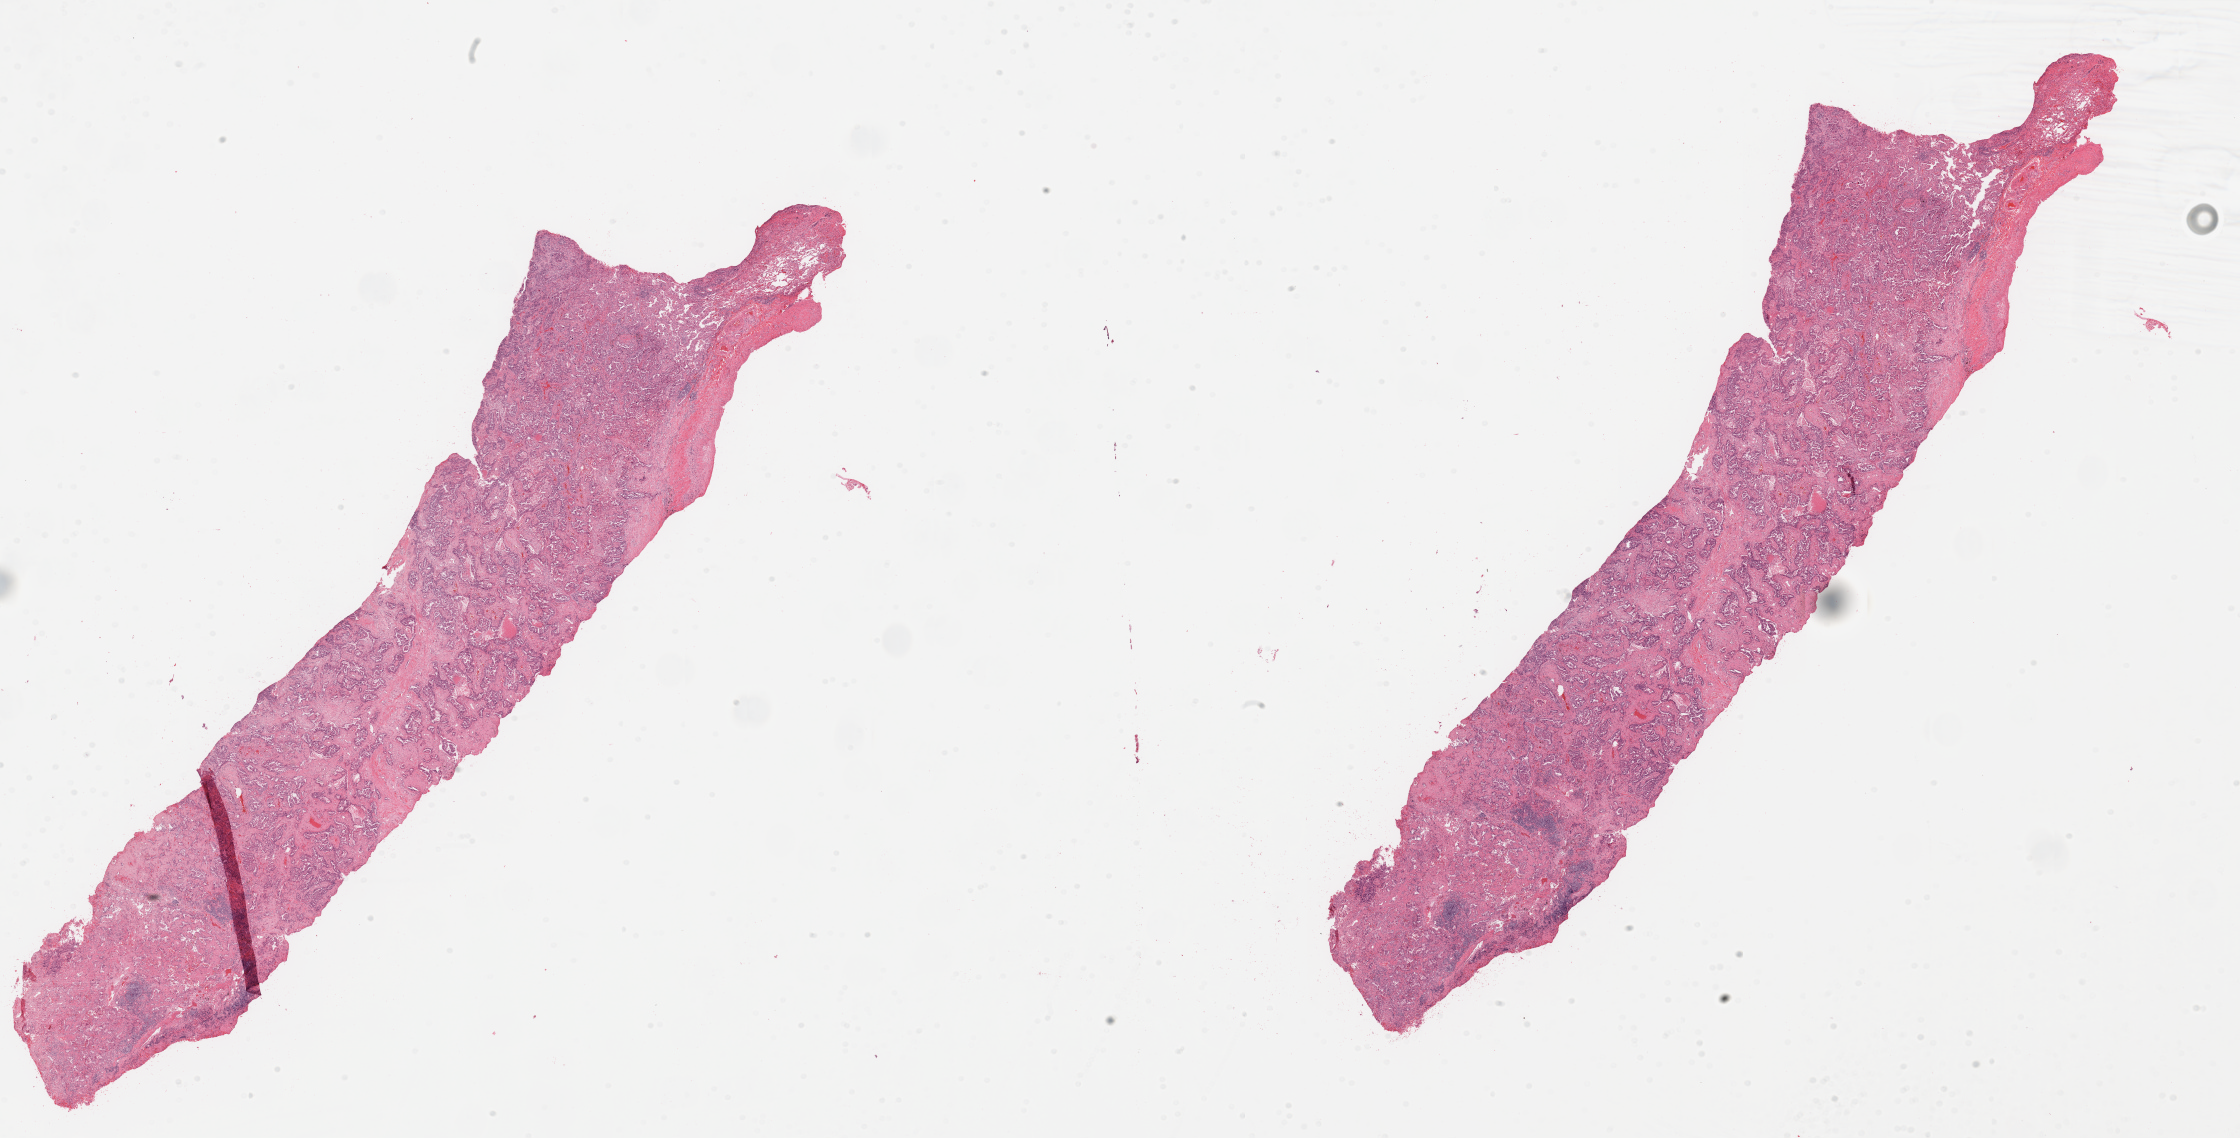
H&E-stained whole-slide image, low-resolution overview of the scanned area, about 35.4 x 18.0 mm (slide scanned at 20x), tumour tissue sample, sampled site: lung. Patient: male, age 65 years. Histologic grade: G2 (moderately differentiated). Composition of this section per pathologist review: tumour nuclei 70%, necrosis 5%.
AJCC pathologic stage: IA. Histologic diagnosis: Adenocarcinoma, NOS. Primary tumour site (as recorded): left upper lobe.